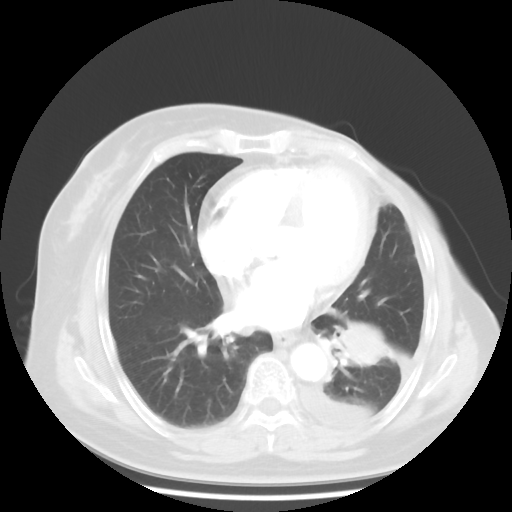
Chest CT, one axial slice; slice 19 of 48 in the series (ordered by position); reconstruction kernel STANDARD; lung window (W 1500 / L -600 HU); 5 mm slice thickness; 512 × 512 image matrix, field of view 360 × 360 mm. Patient: female, 63 years. From the clinical record (not read from this slice): clinical TNM (as recorded): T2 N0 M1.
Structures marked on this image (rectangle marked by the reading radiologist):
- lung tumour (recorded histology: adenocarcinoma): box from (x=329, y=306) to (x=392, y=370) px